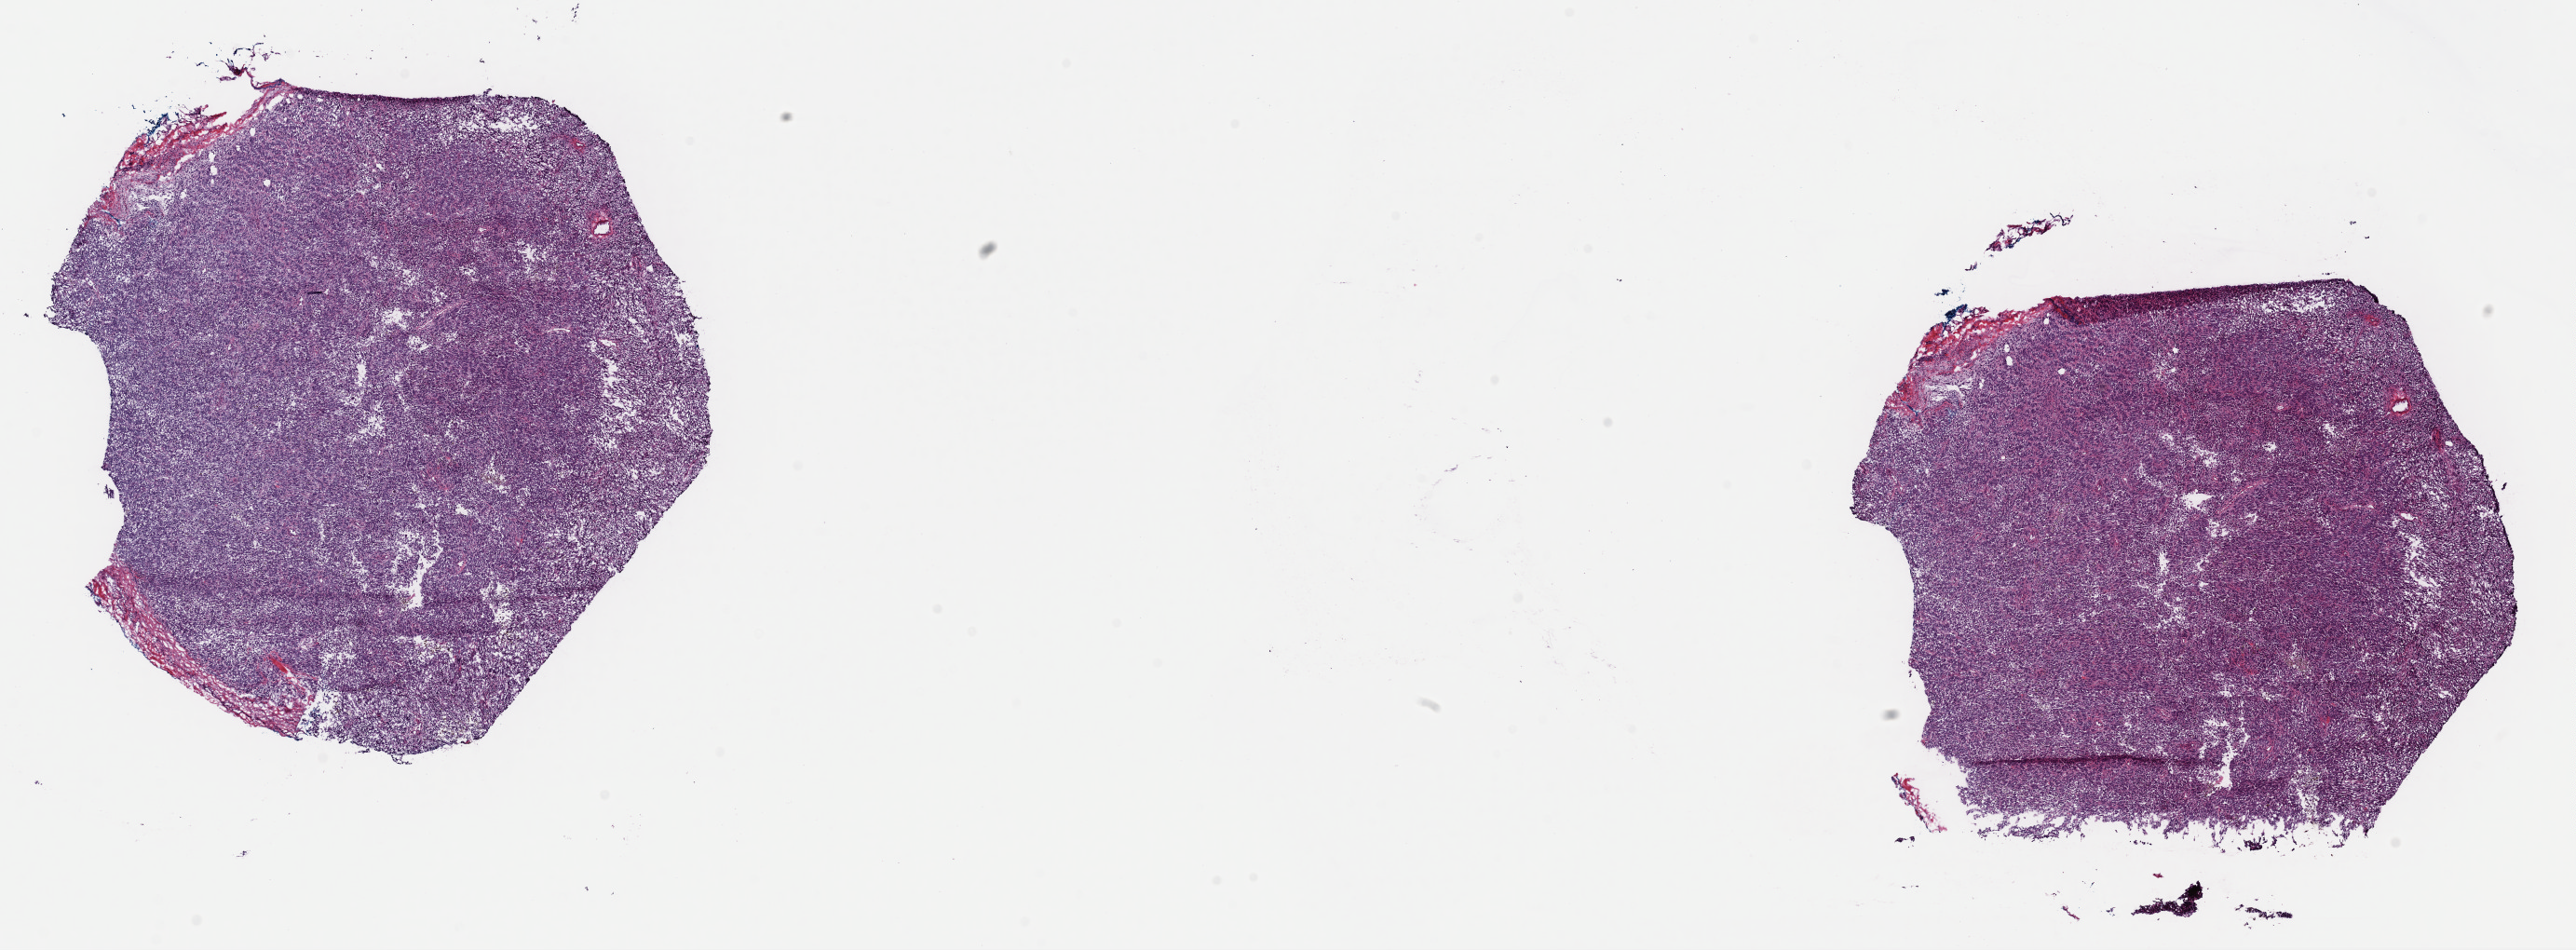
Digitized H&E tissue section (whole slide) — shown as a low-resolution overview of the whole scanned area (about 21.9 x 8.1 mm, acquisition: 40x scan); frozen section from the top of the tissue portion; metastatic tumour sample, sampled site: lymph nodes of head, face and neck. Patient: male, age at initial diagnosis 87 years.
This section: metastatic tumour tissue. Patient diagnosis: Malignant melanoma, NOS.